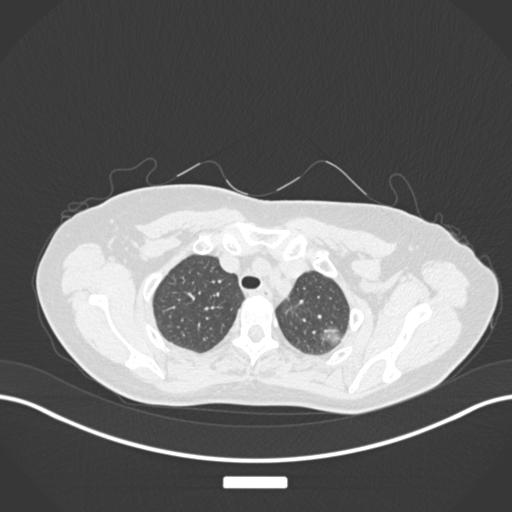
Chest CT, one axial slice; slice 144 of 181 in the series (ordered by position); reconstruction kernel B30f; 120 kVp; lung window (W 1500 / L -600 HU); 1 mm slice thickness; 512 × 512 image matrix. Patient: female, 58 years. Case-level facts recorded for this patient, not image findings: clinical TNM (as recorded): T1c N0 M0.
Structures marked on this image (rectangle marked by the reading radiologist):
- lung tumour (recorded histology: adenocarcinoma): bounding box <318,325,346,348> (left, top, right, bottom; pixels)